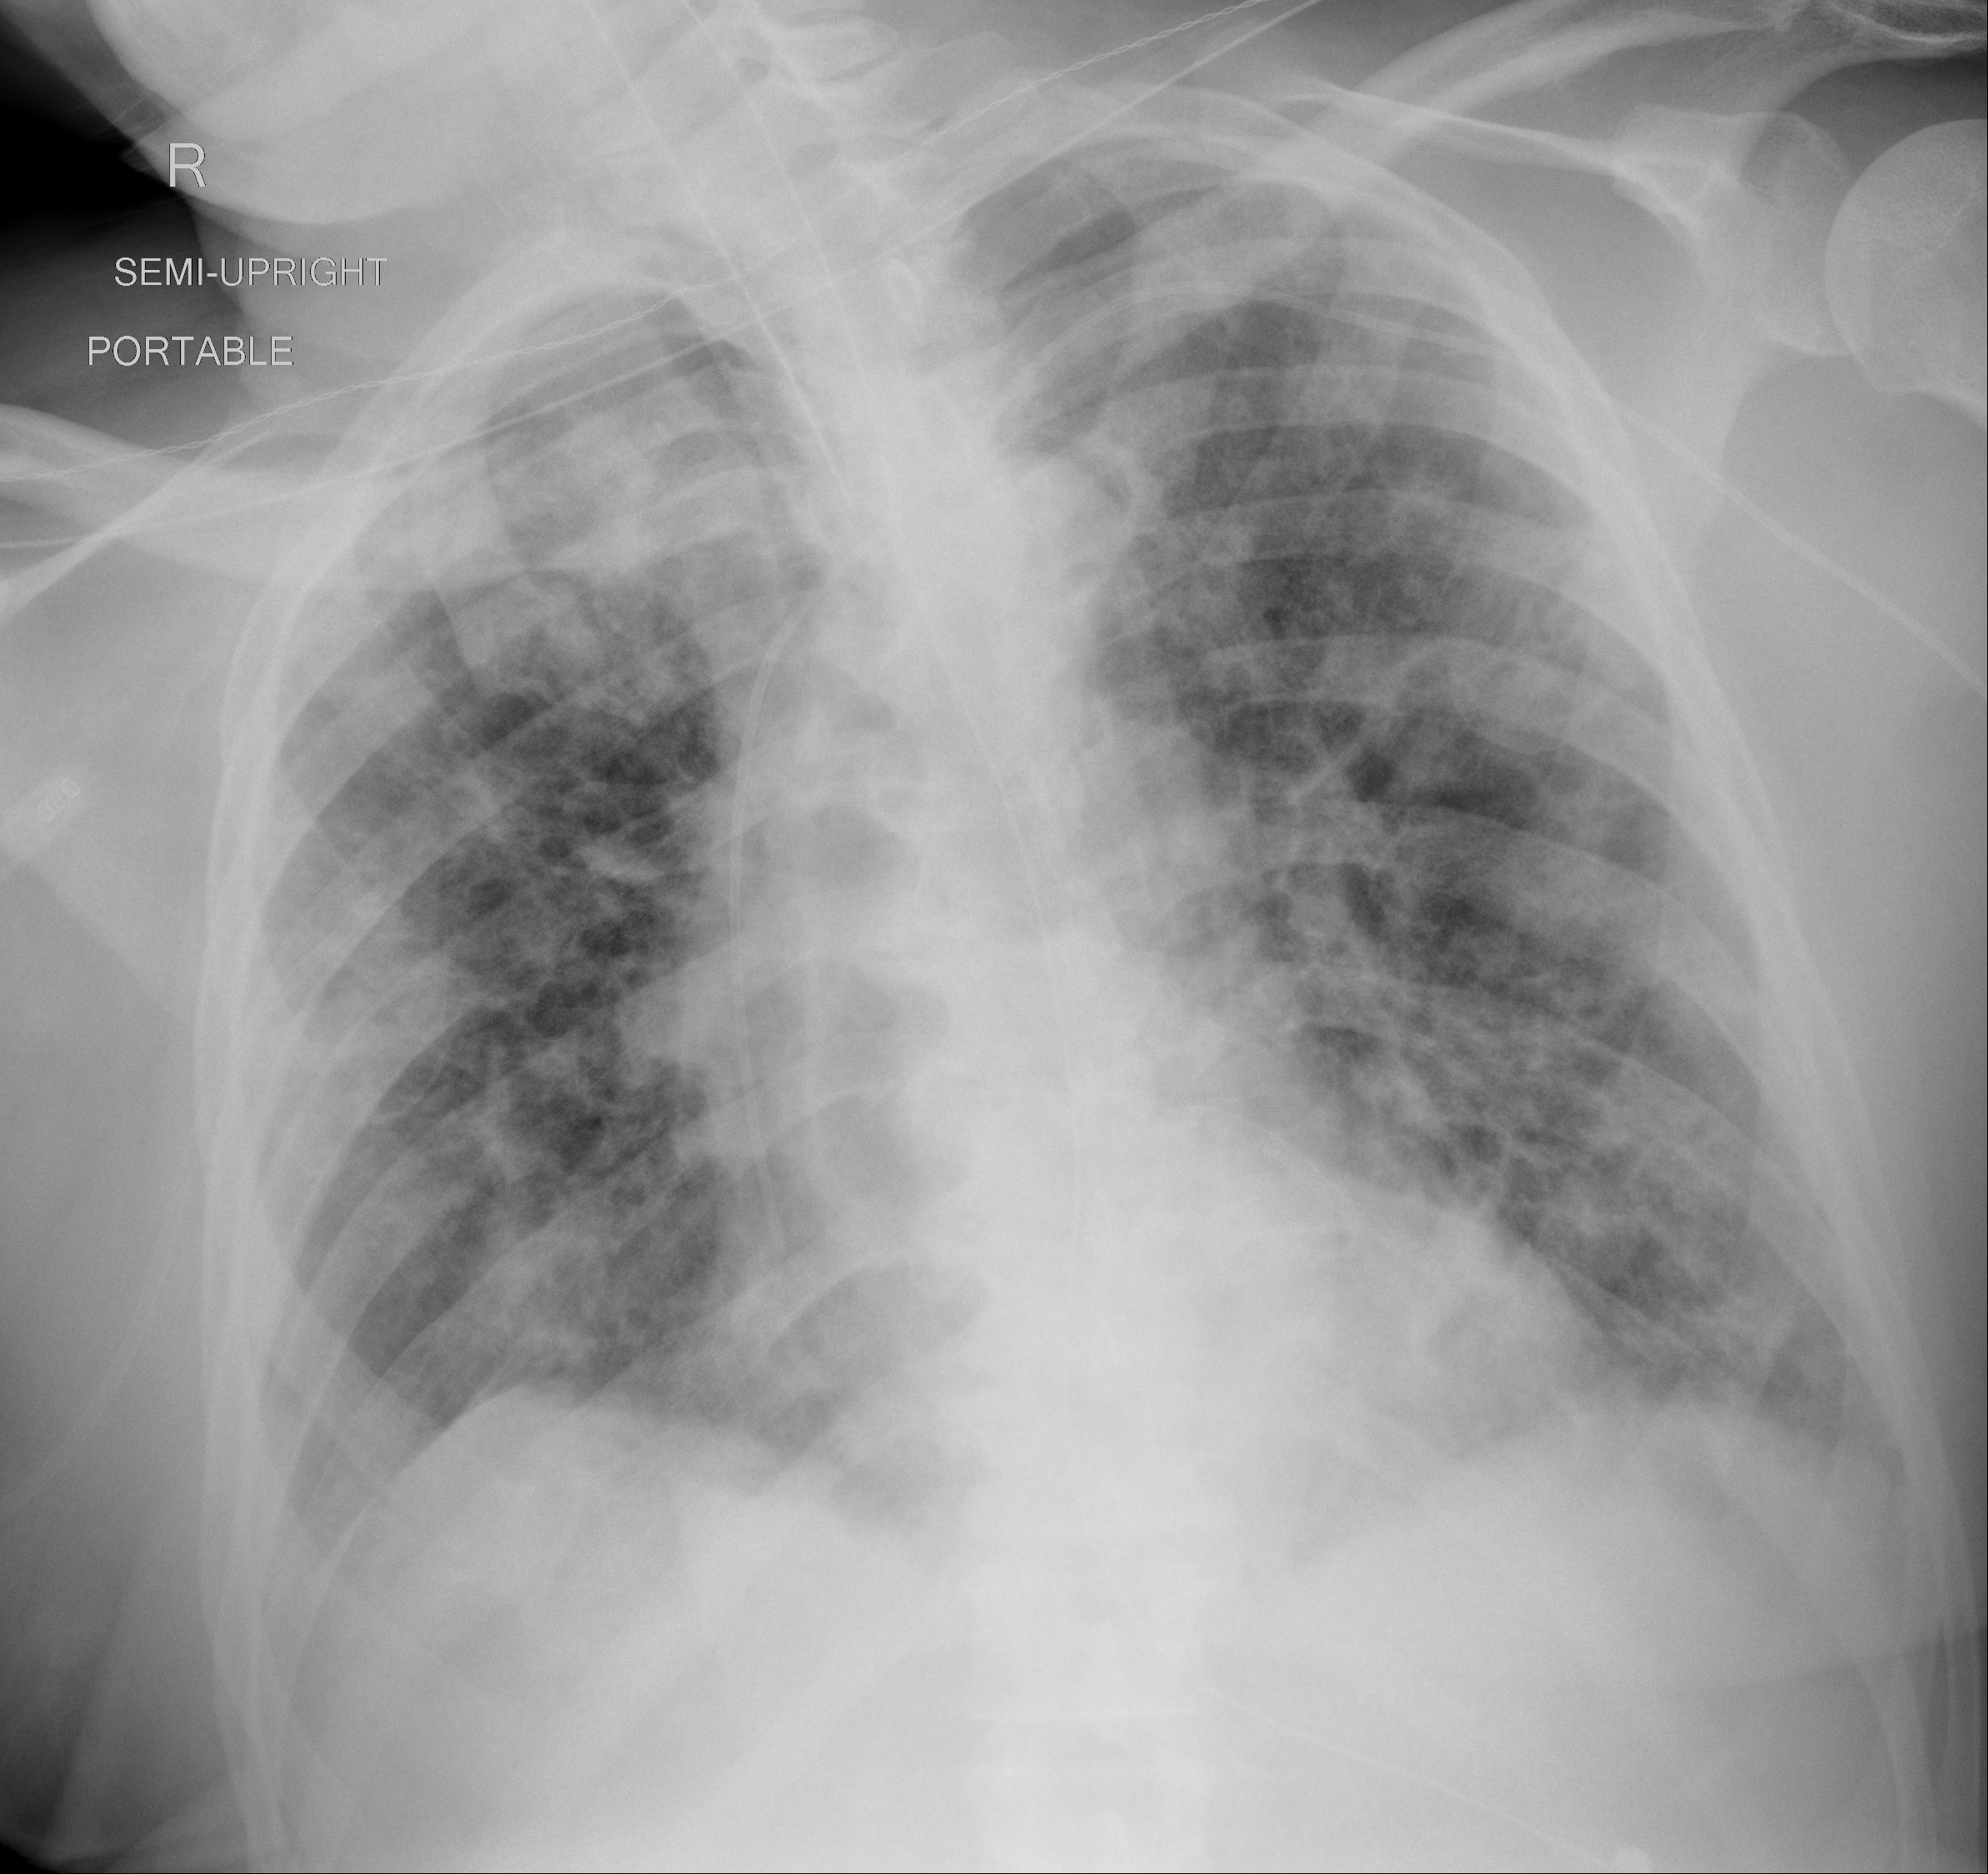
Chest X-ray (portable), AP projection. Male patient, age 64 years; COVID-19 (test-positive).
Radiologist key findings (as recorded): No improvement in the diffuse bilateral patchy infiltrates.